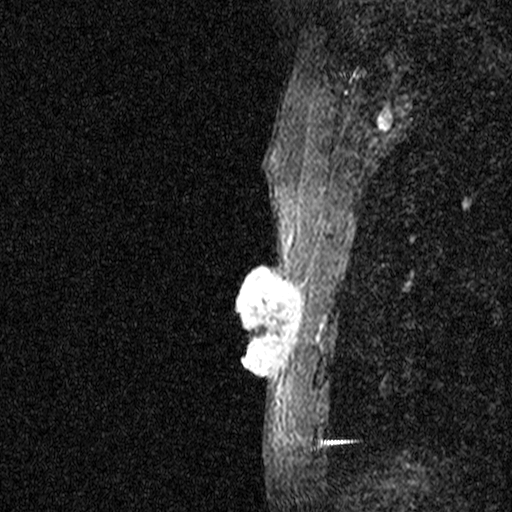
Breast MRI (dynamic contrast-enhanced), one sagittal slice. Slice 38 of 44 in the series (ordered by position). Dynamic contrast-enhanced study with each time point stored as its own series, time point 2 of 3 at this slice position (early post-contrast, ordered by acquisition time). 1.5 T. TE 4.5 ms, TR 11 ms. 512 × 512 image matrix, field of view 200 × 200 mm. Patient: female, 44 years. Case-level facts recorded for this patient, not image findings: setting: breast cancer imaged before/during neoadjuvant chemotherapy; receptor status: HR-positive, HER2-negative.
Outlined on this slice (semi-automatic segmentation, software-assisted and operator-edited):
- analysis volume of interest (the breast-tissue region the enhancement analysis was run in; not a lesion): box from (x=204, y=254) to (x=314, y=401) px
- tumour enhancement mask (voxels above the 90 % enhancement threshold inside the analysis volume of interest): (x=236, y=254)–(x=300, y=390)